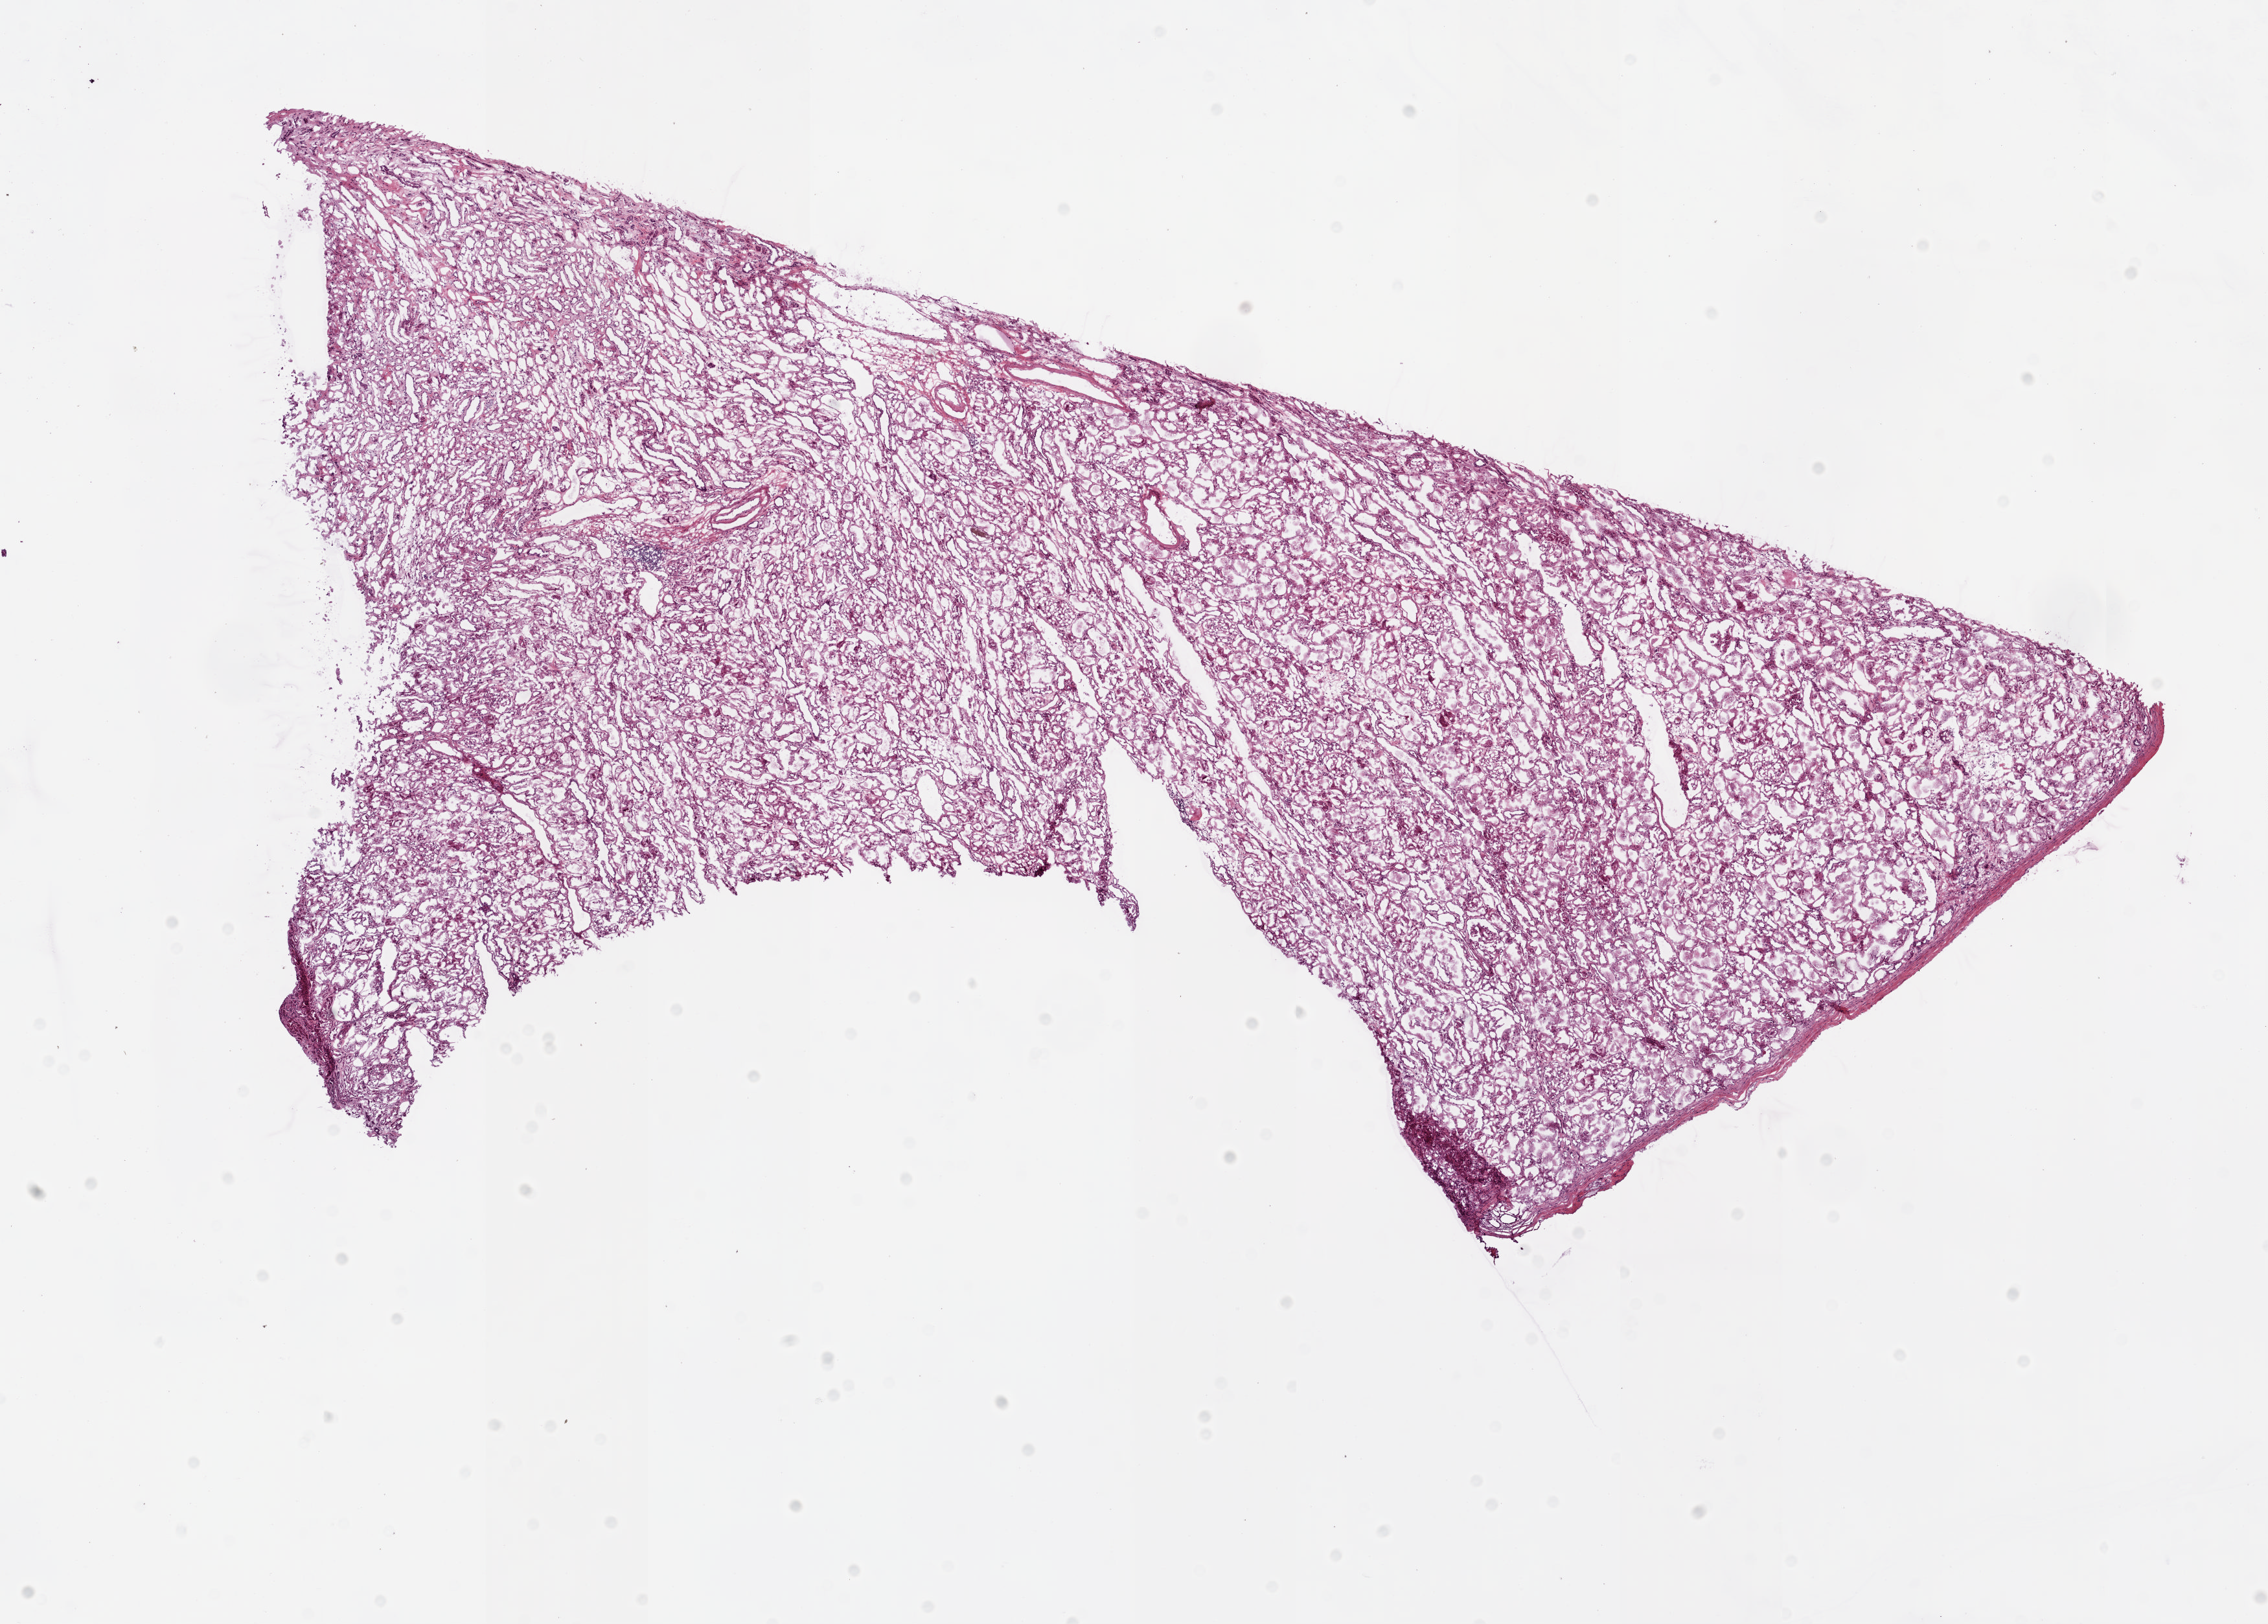
Whole-slide histology image, H&E, whole scanned area (about 13.9 x 9.9 mm) shown as a low-resolution overview. Frozen section. Sample: solid tissue normal (non-tumour tissue), kidney. Male patient; age at initial diagnosis 75 years.
* this section: solid tissue normal (non-tumour) sample from the same patient
* patient diagnosis: Clear cell adenocarcinoma, NOS